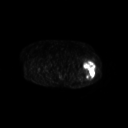
FDG PET of an extremity soft-tissue mass (from a PET/CT study), one axial slice. Position 249 of 267 along the scan axis. 3.27 mm slice thickness. 128 × 128 image matrix. Patient: female, 62 years. Case-level facts recorded for this patient, not image findings: histological type: undifferentiated – high grade; grade: high; site of the primary tumour: left thigh.
Annotated regions visible in this slice (expert contour drawn on MRI and transferred to this co-registered scan by the dataset authors):
- gross tumour volume including surrounding oedema: box from (x=83, y=60) to (x=95, y=80) px
- gross tumour volume (mass): (x=83, y=61)–(x=95, y=80)